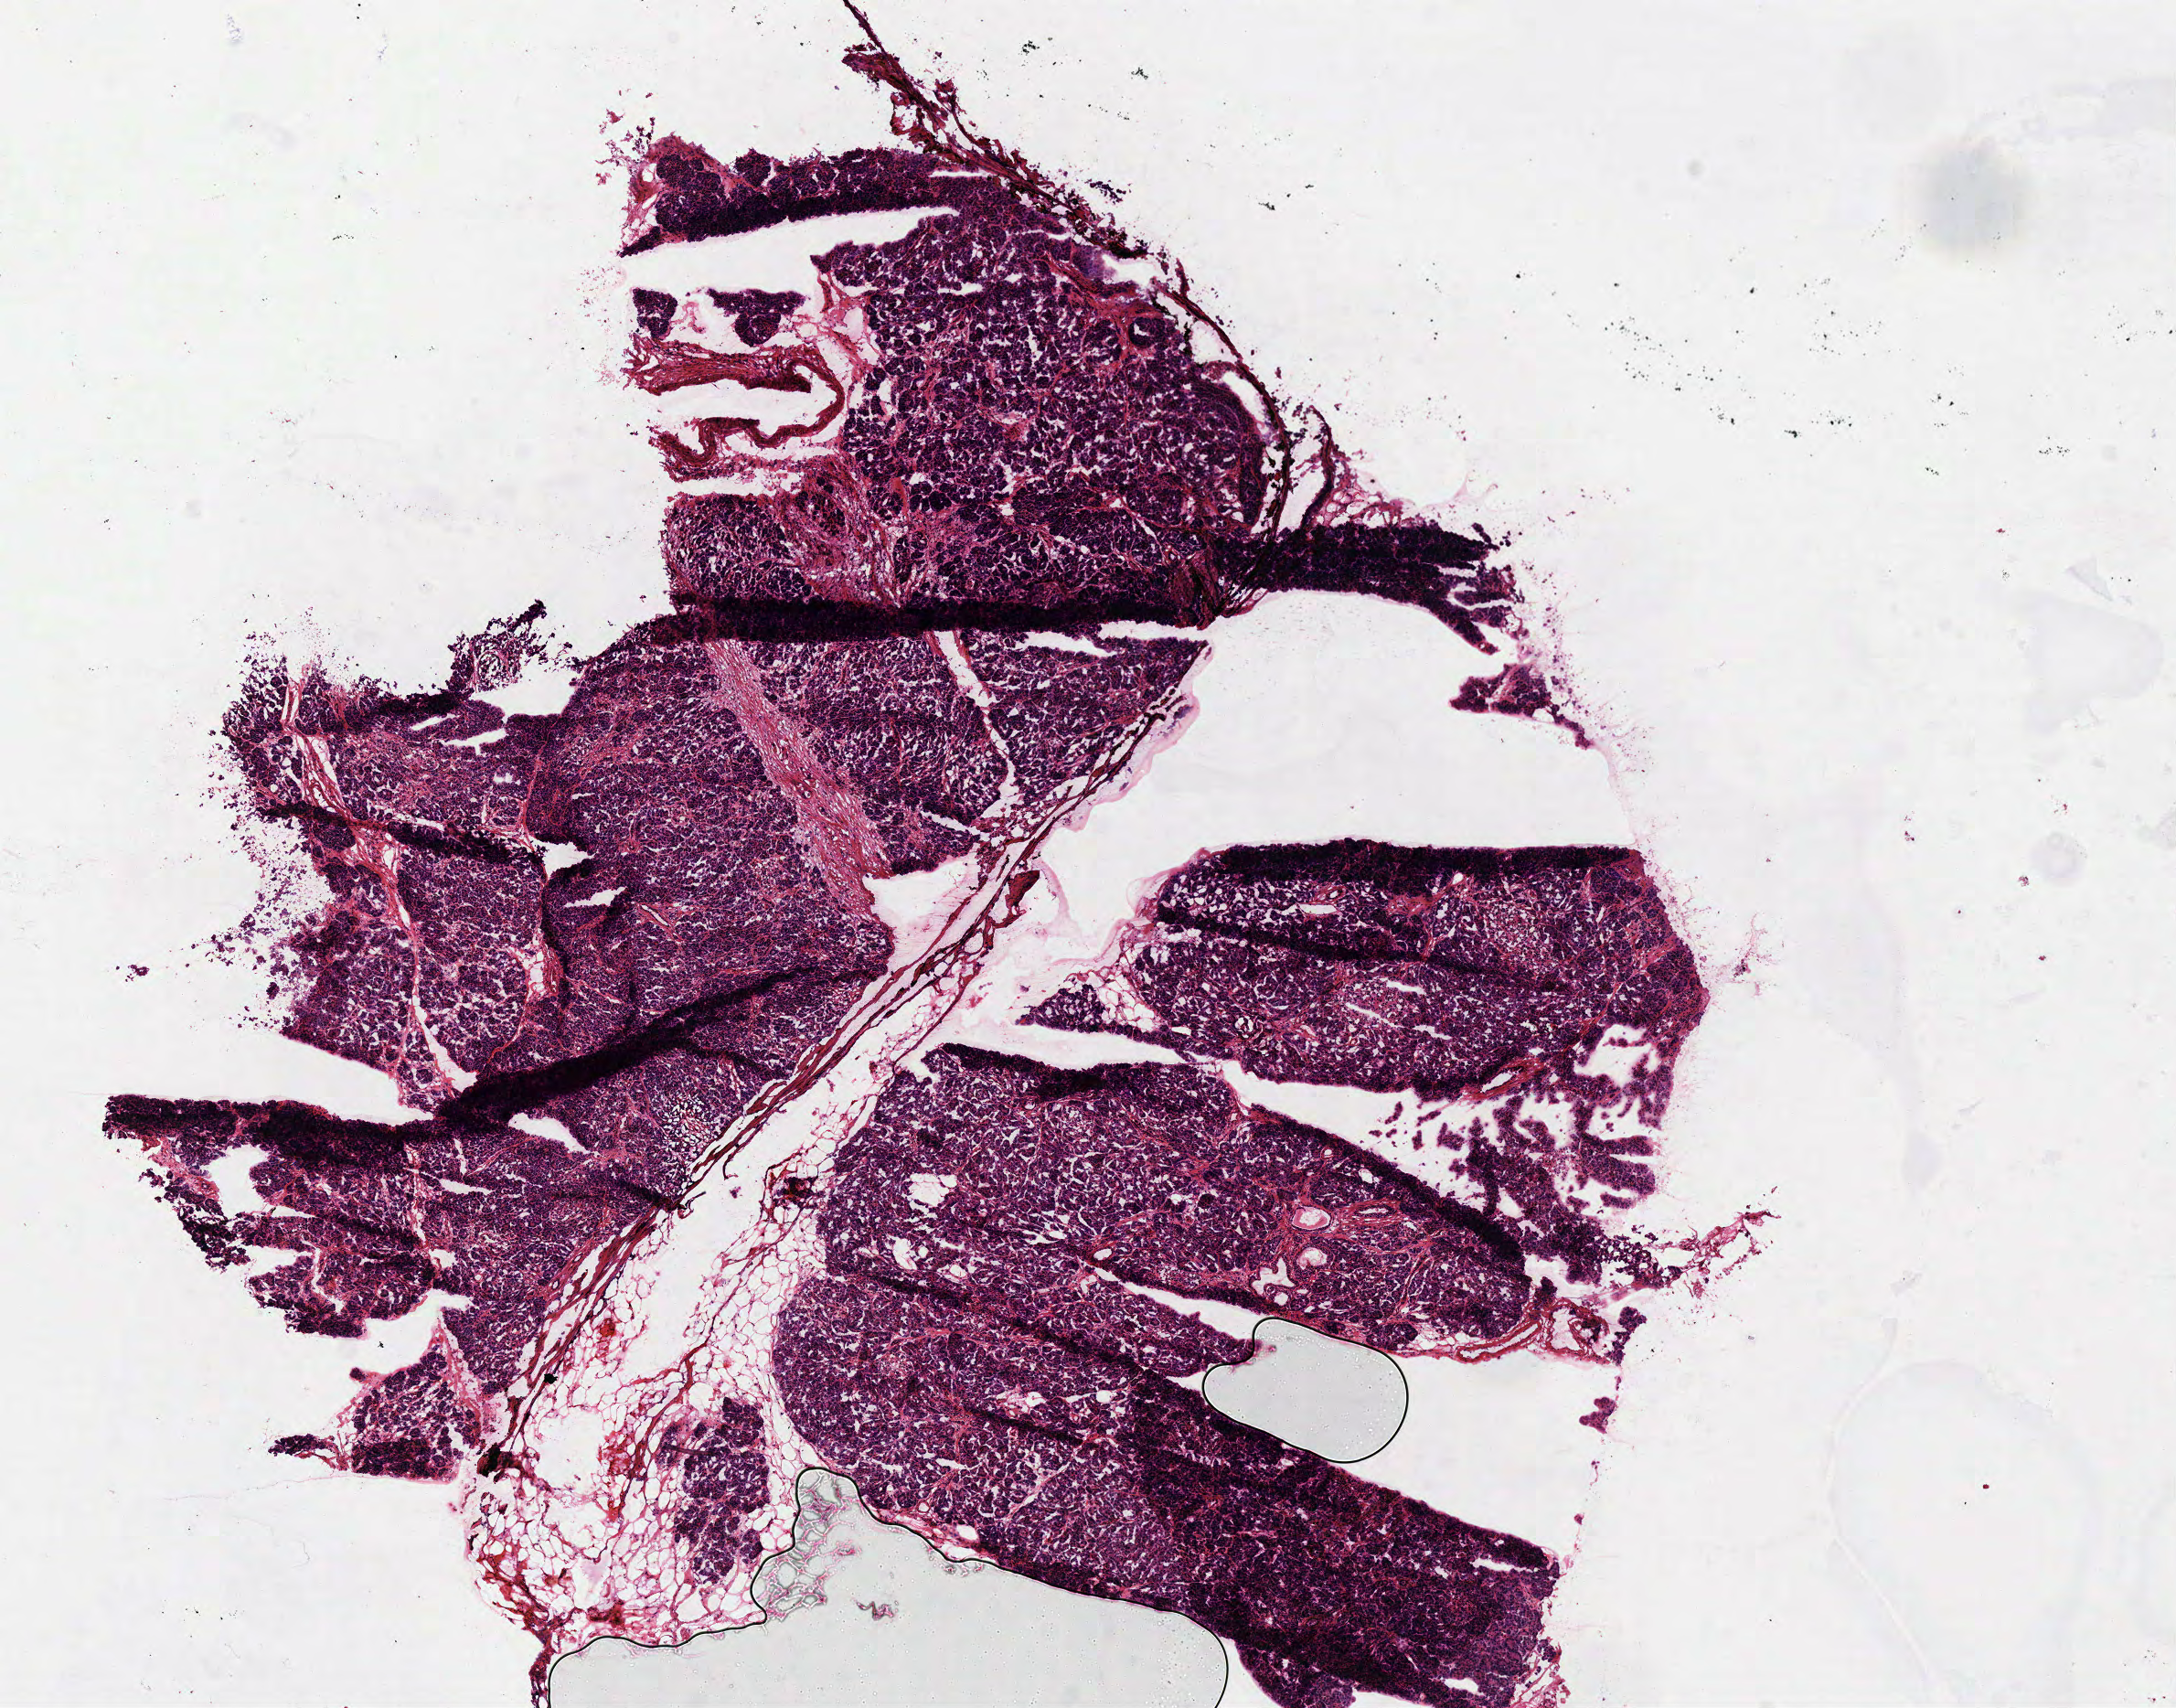
H&E-stained whole-slide image — a low-resolution overview of the entire scanned area, about 9.4 x 7.4 mm. Frozen section. Sample: solid tissue normal (non-tumour tissue), pancreas. Female, age 73 years at initial diagnosis.
* this section: solid tissue normal sample (biorepository sample class)
* patient diagnosis: Infiltrating duct carcinoma, NOS (head of pancreas)